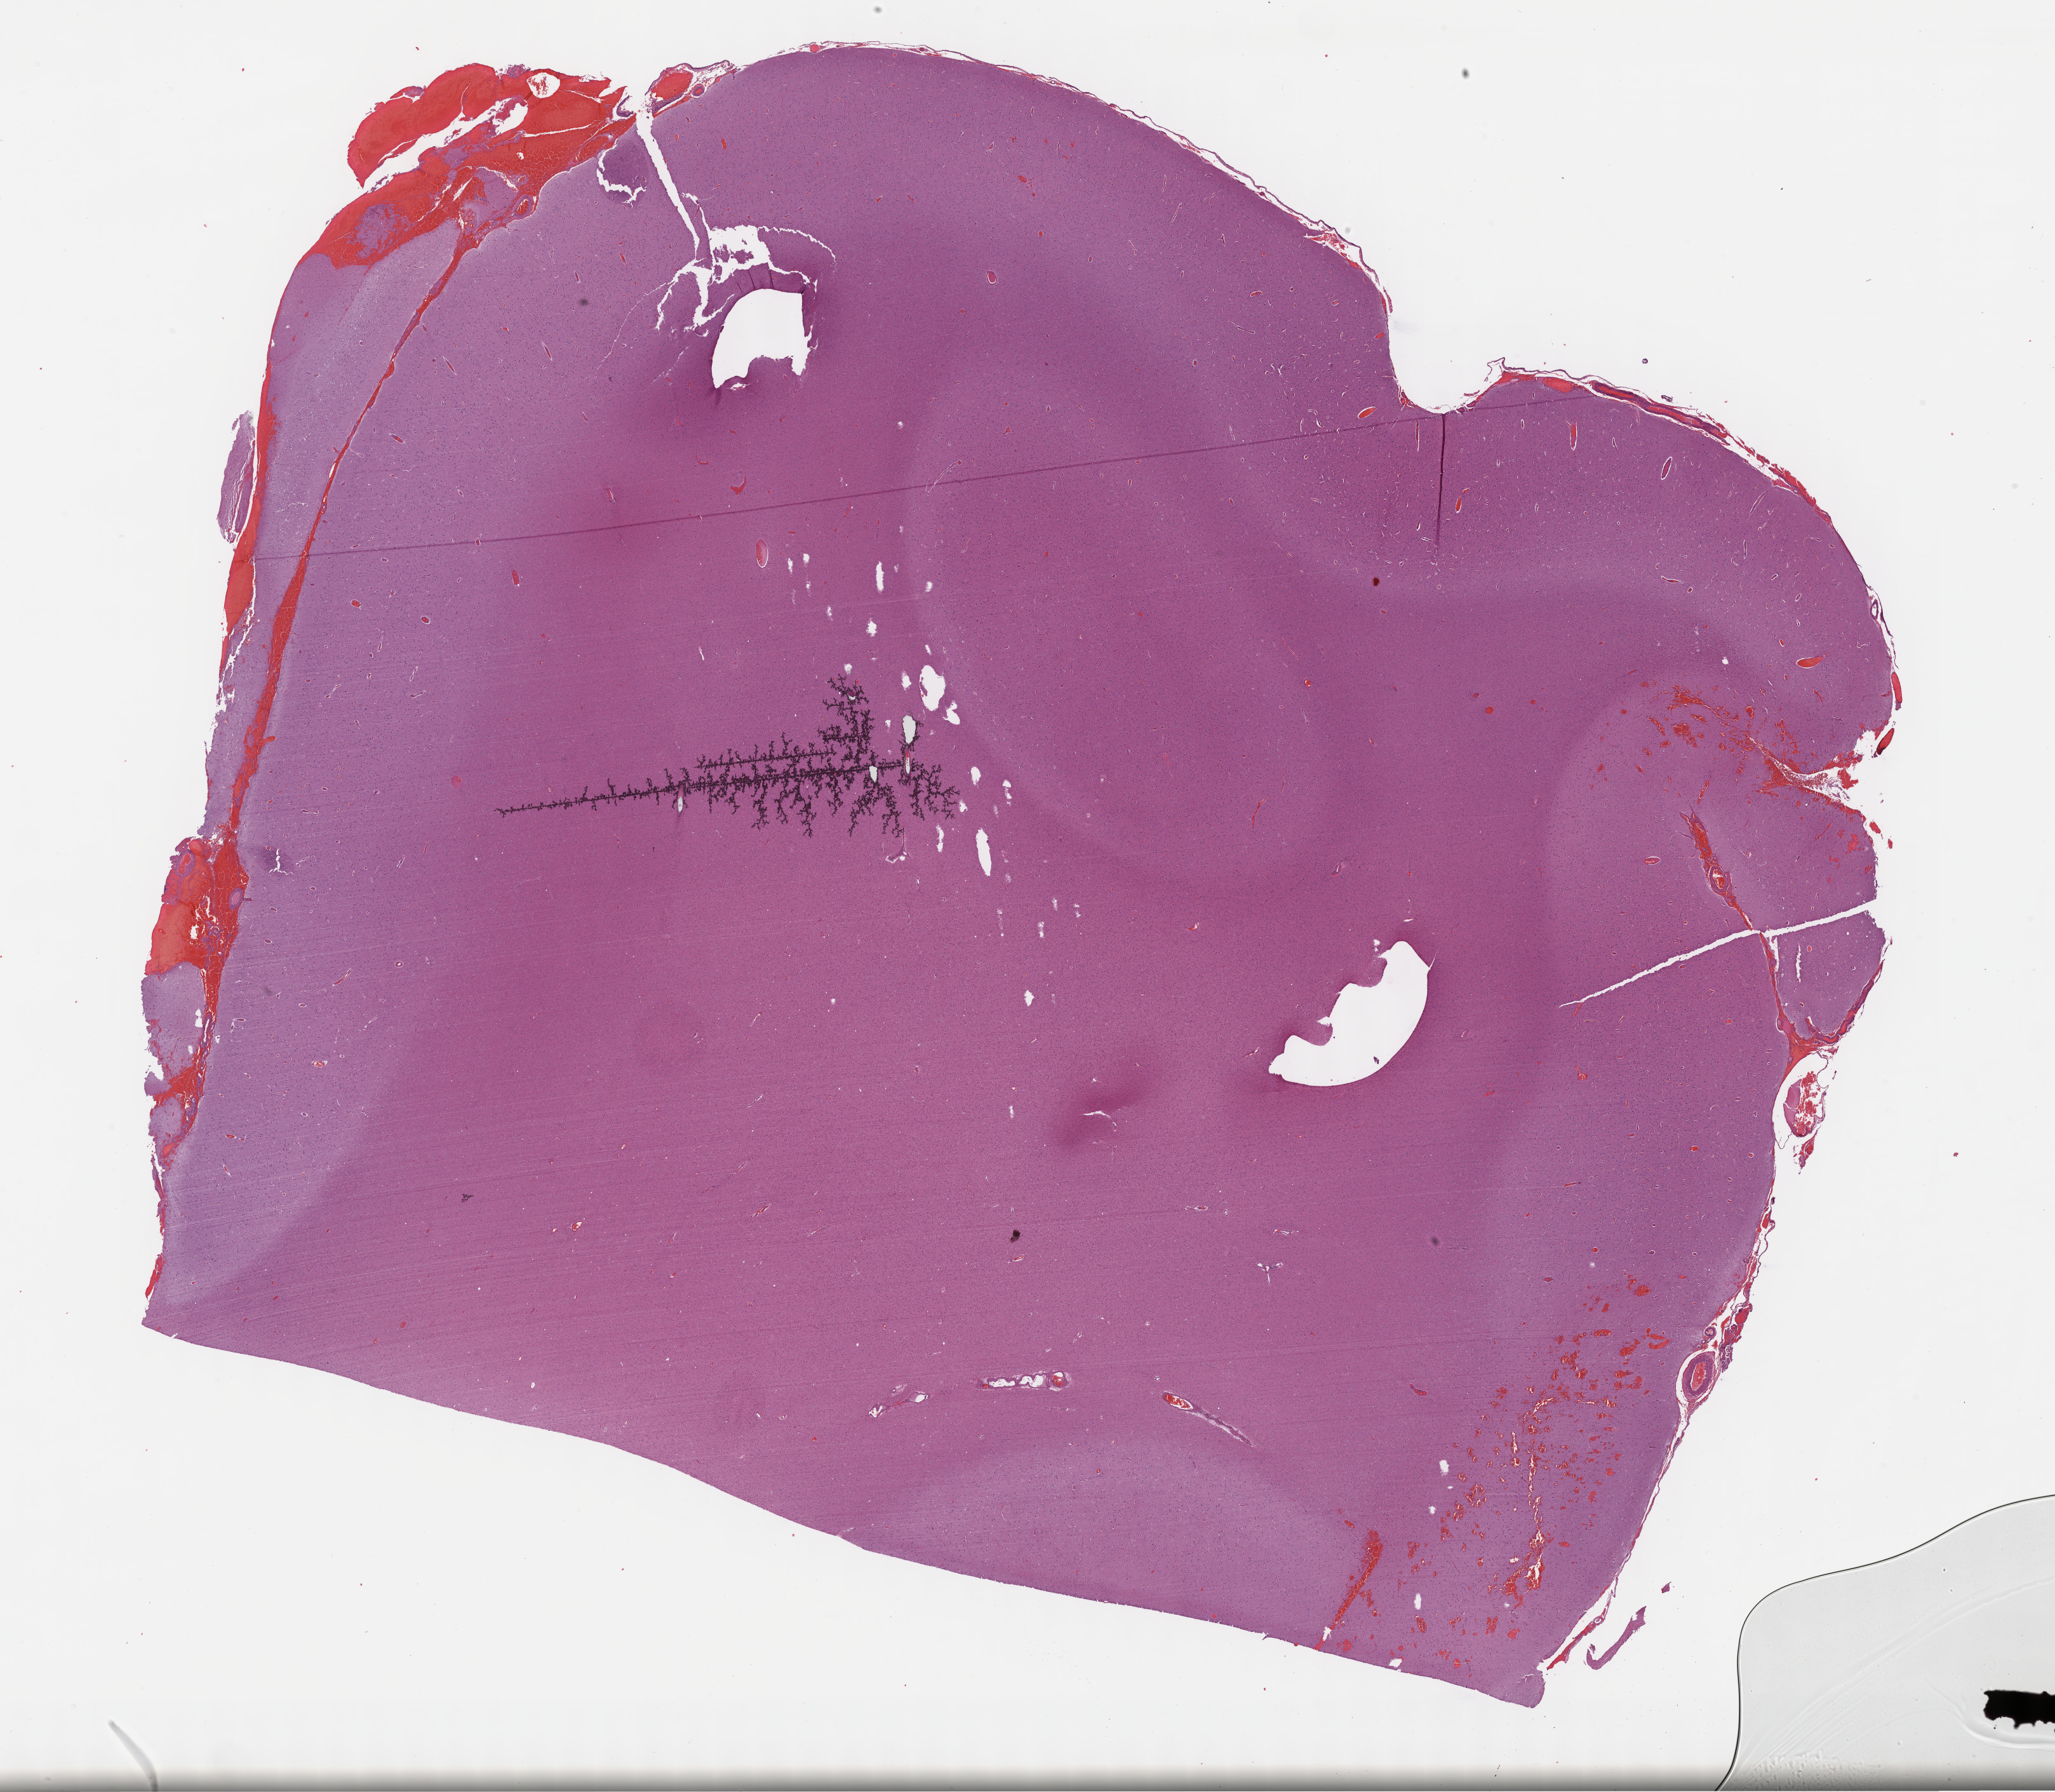
Whole-slide histology image, H&E-stained, low-resolution overview of the scanned area, about 26.2 x 22.8 mm, formalin-fixed paraffin-embedded (FFPE) diagnostic section, sample: primary tumour, brain. Male, age 61 years at initial diagnosis. Histologic grade: G2 (moderately differentiated).
* laterality: right
* pathologic diagnosis: Mixed glioma (cerebrum)